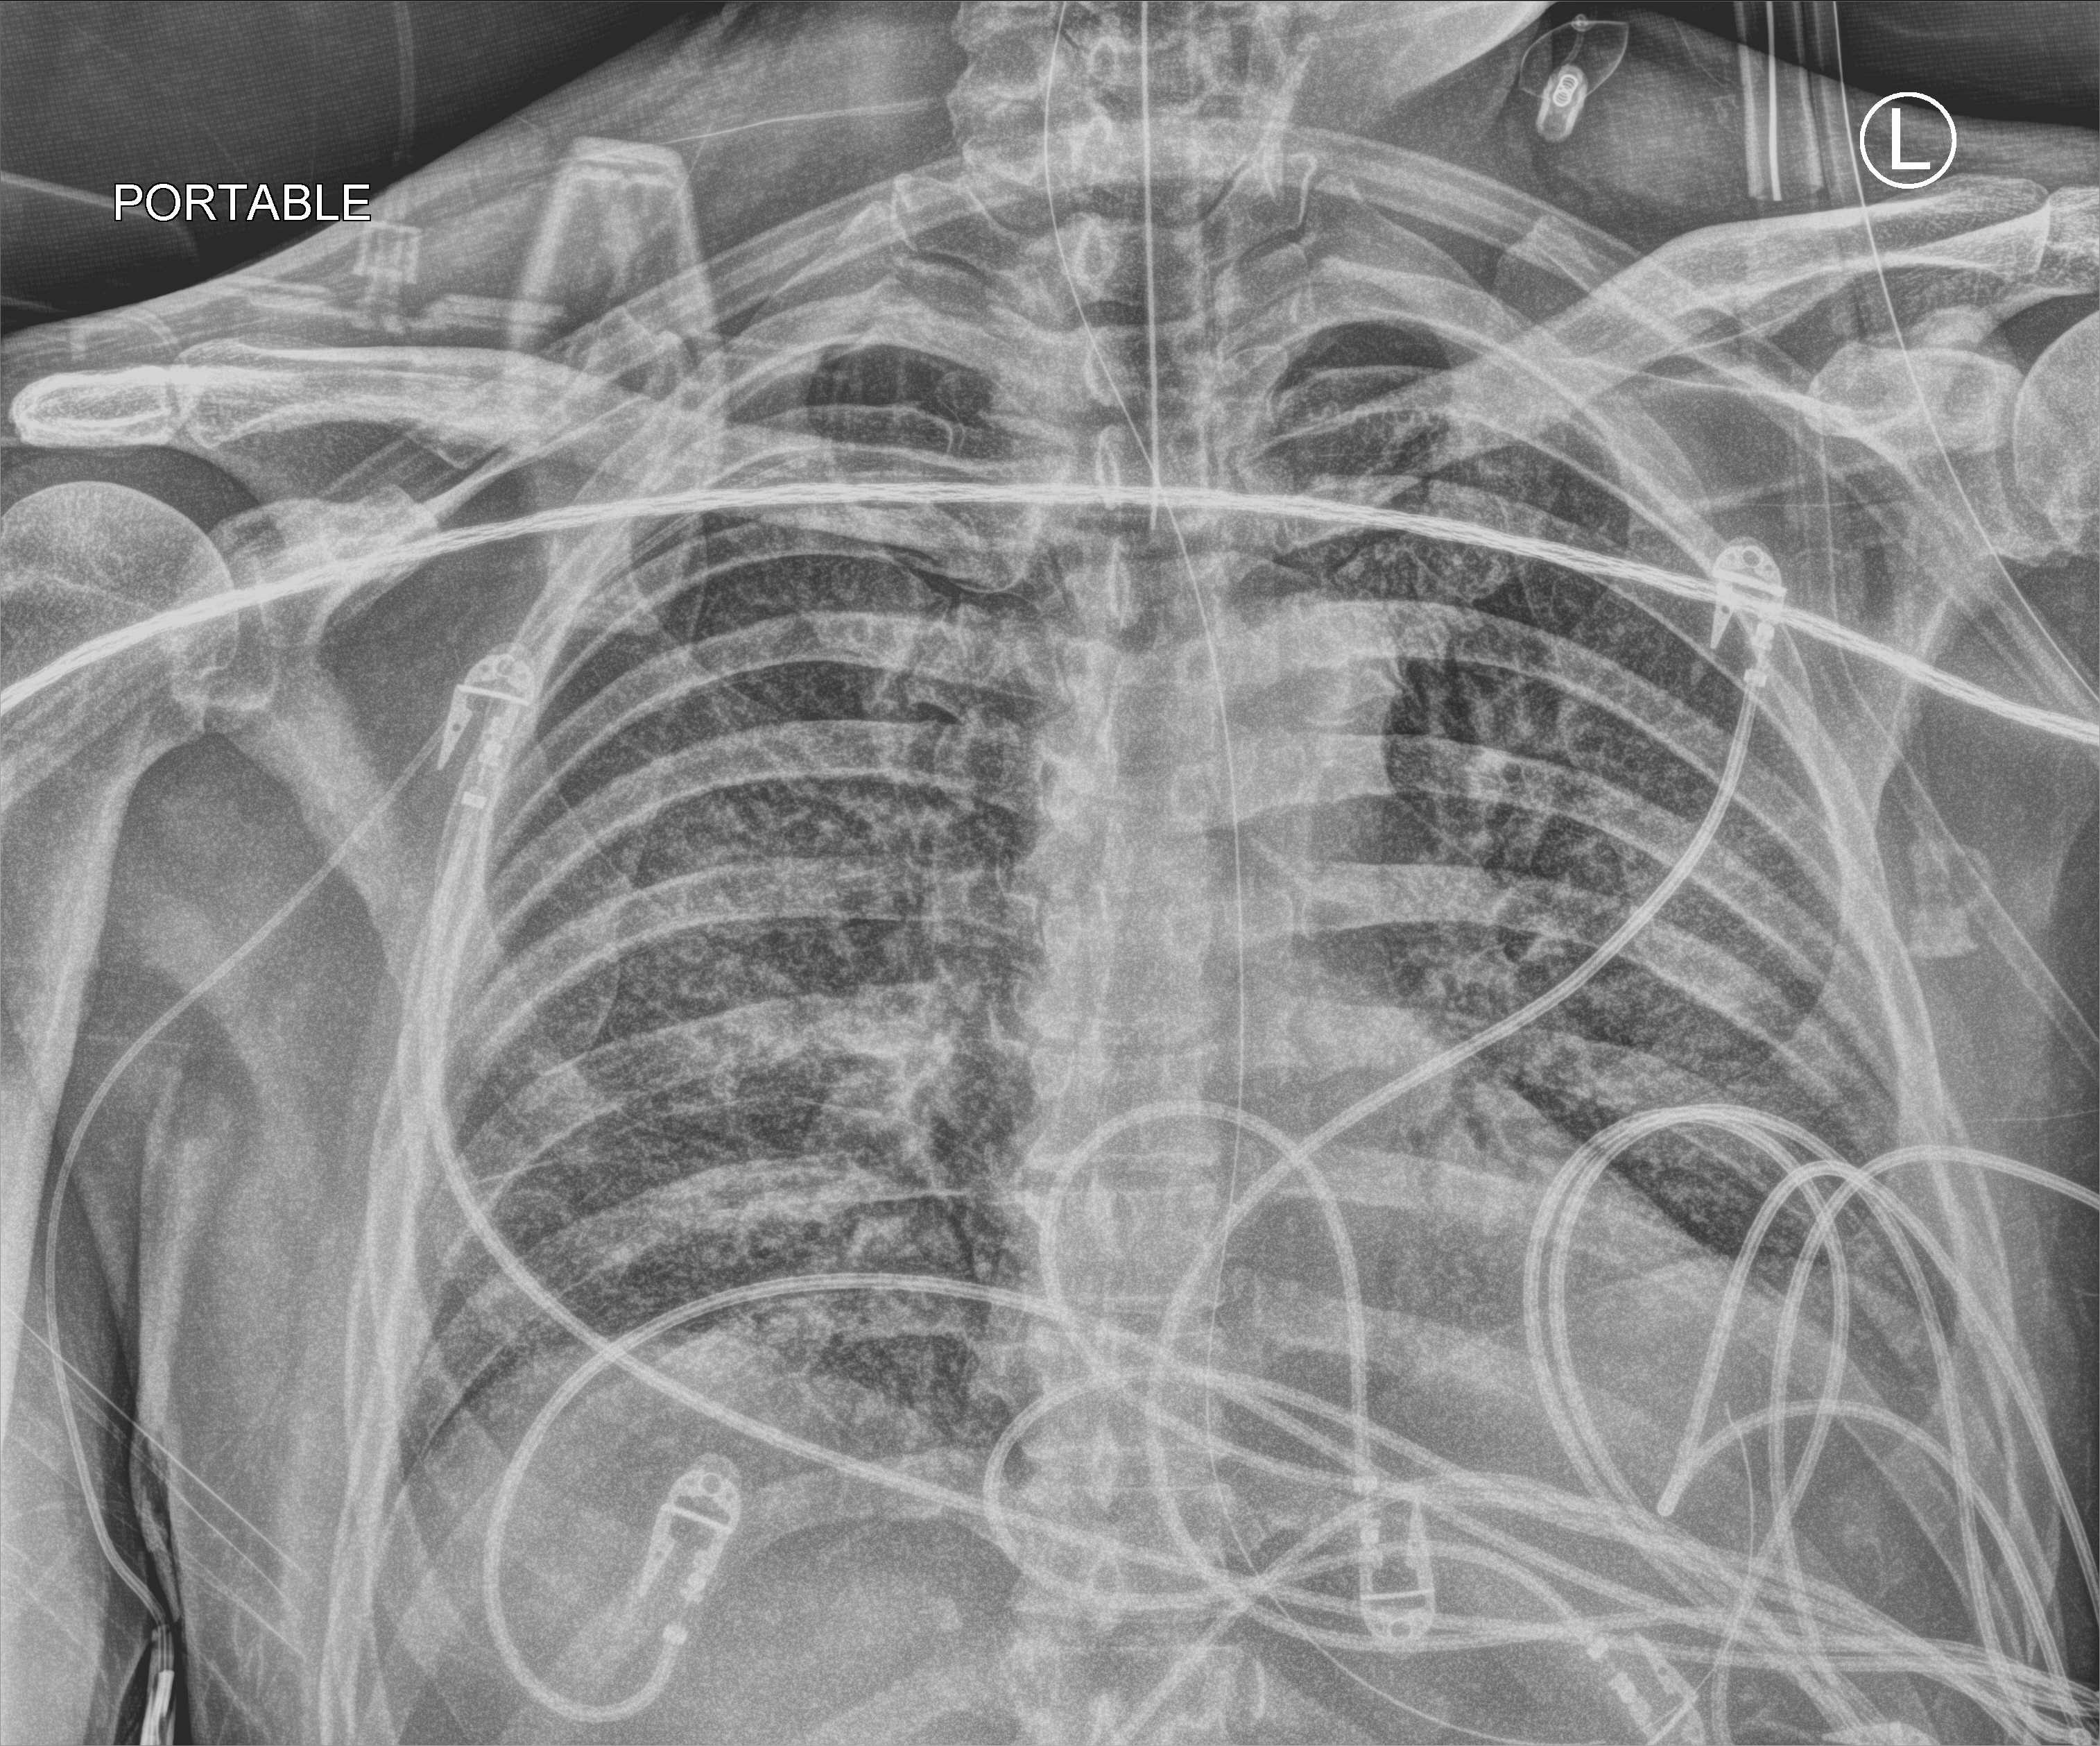
Chest X-ray (portable), anteroposterior (AP) projection. Patient hospitalised with COVID-19; male, aged 60–74 years.
From the hospital-stay record, not from the radiograph (when in the stay this image was taken is not recorded): chronic kidney disease (admission record): no.